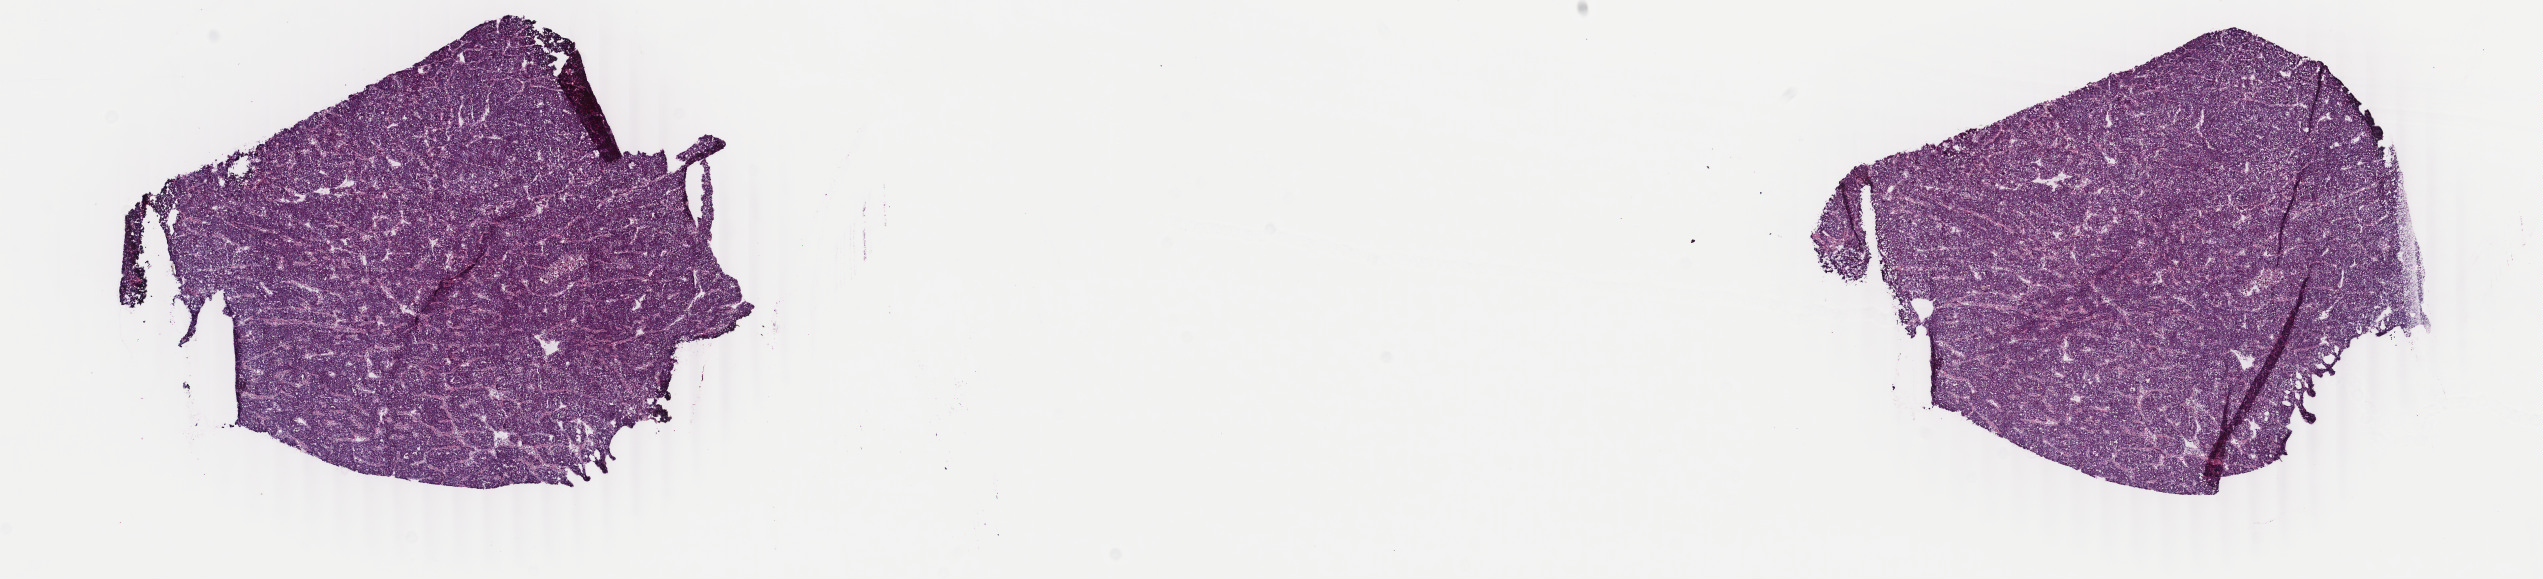
Whole-slide histology image, Hematoxylin and eosin (H&E) stained, shown as a low-resolution overview of the whole scanned area (about 20.2 x 4.6 mm, slide scanned at 40x), frozen section from the top of the tissue portion, sample: primary tumour, liver. Male patient; age at initial diagnosis 51 years. Histologic grade: G3 (poorly differentiated). Composition of this section per pathologist review: tumour cells 100%, tumour nuclei 75%, normal cells 0%, stromal cells 0%, necrosis 0%. Infiltration values recorded for this section: lymphocyte infiltration 2%, monocyte infiltration 0%, neutrophil infiltration 0%.
• AJCC pathologic stage: I (7th edition)
• diagnosis: Hepatocellular carcinoma, NOS